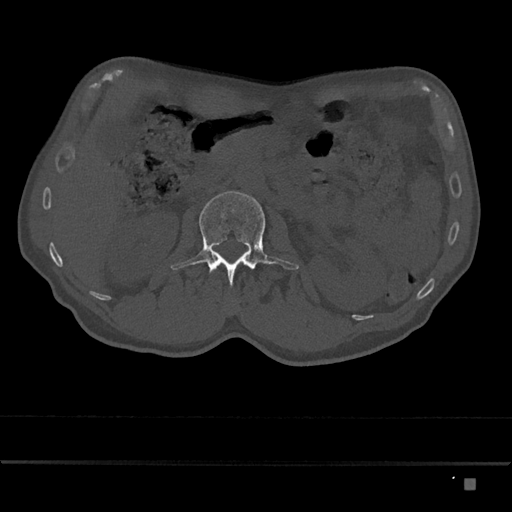
CT including the spine, one axial slice. Reconstruction kernel Br40s/3. Bone window (W 1800 / L 400 HU). 0.5 mm slice thickness. 512 × 512 image matrix, field of view 390 × 390 mm. Patient: male, 72 years. Case-level facts recorded for this patient, not image findings: primary cancer: prostate.
Outlined on this slice (semi-automatically segmented with operator editing):
- L2 vertebra: bounding box [x1, y1, x2, y2] px = [171, 191, 299, 287]